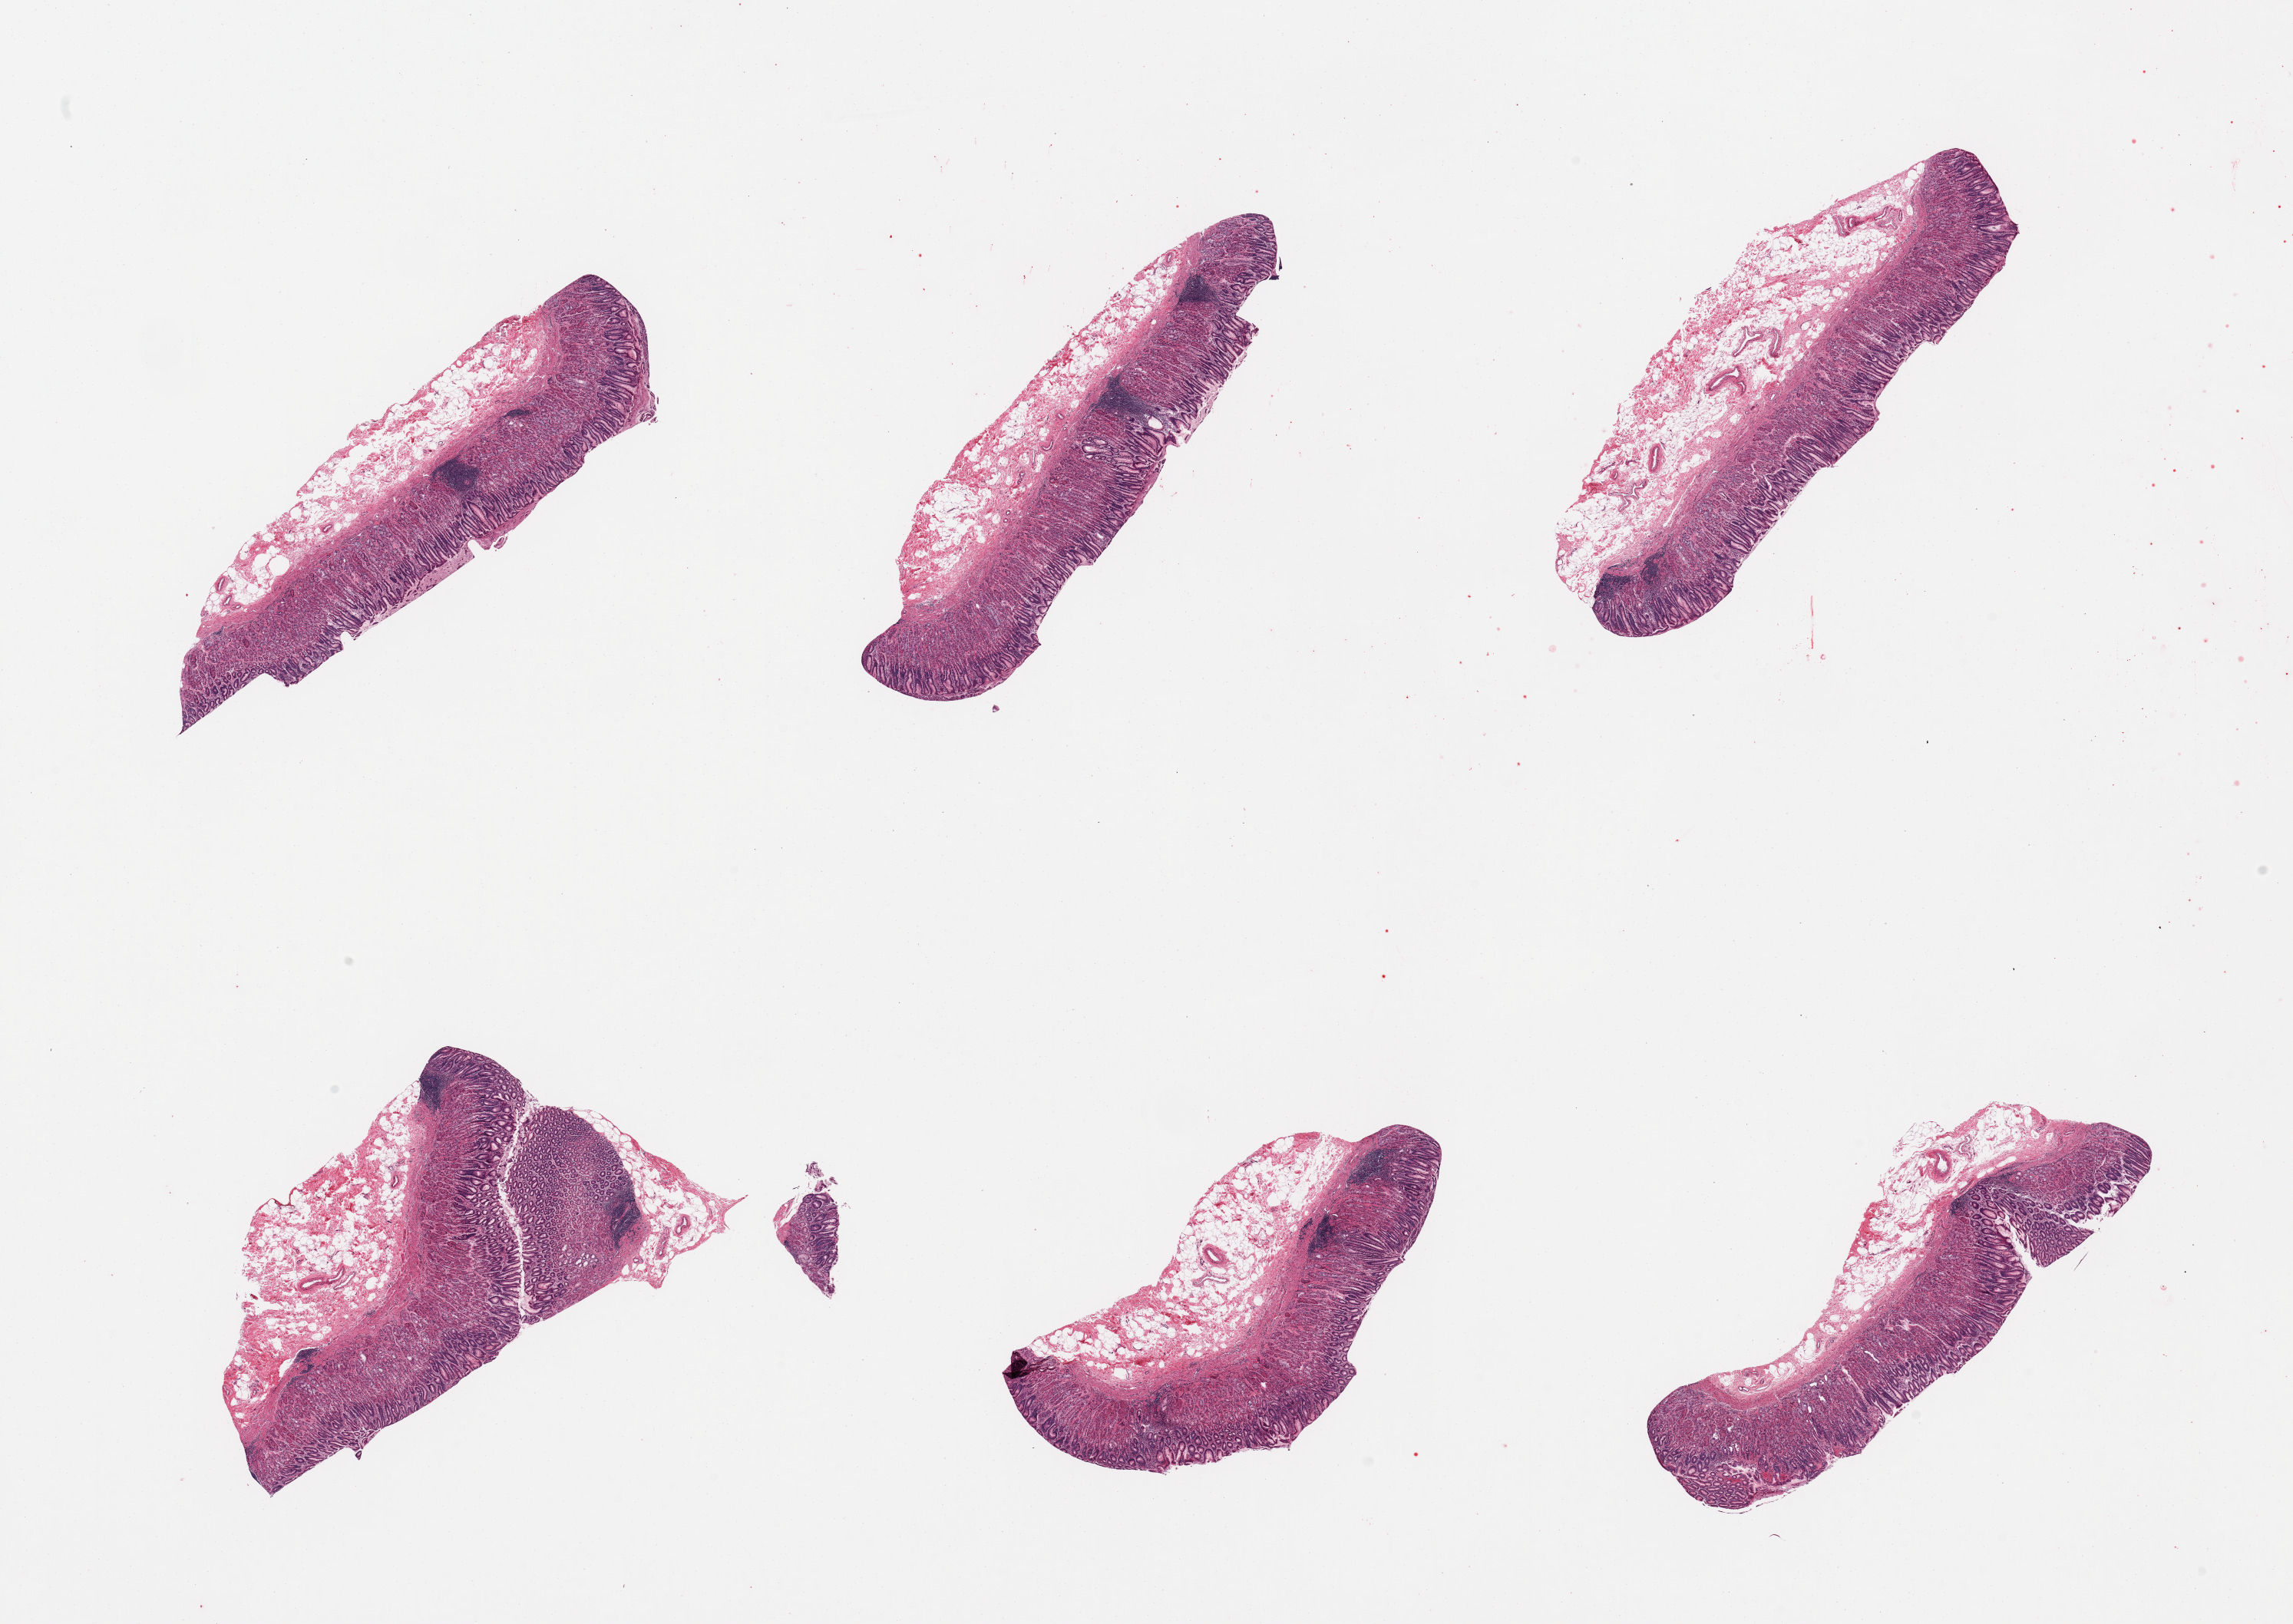
Whole-slide image, hematoxylin and eosin (H&E) stain — shown as a low-resolution overview of the whole scanned area (about 23.6 x 16.7 mm); PAXgene-fixed, paraffin-embedded tissue; sampled site (target tissue): gastroesophageal junction; donor tissue sample. Donor: male.
- pathologist's review note for this sample: 6 pieces; all are gastric mucosa only